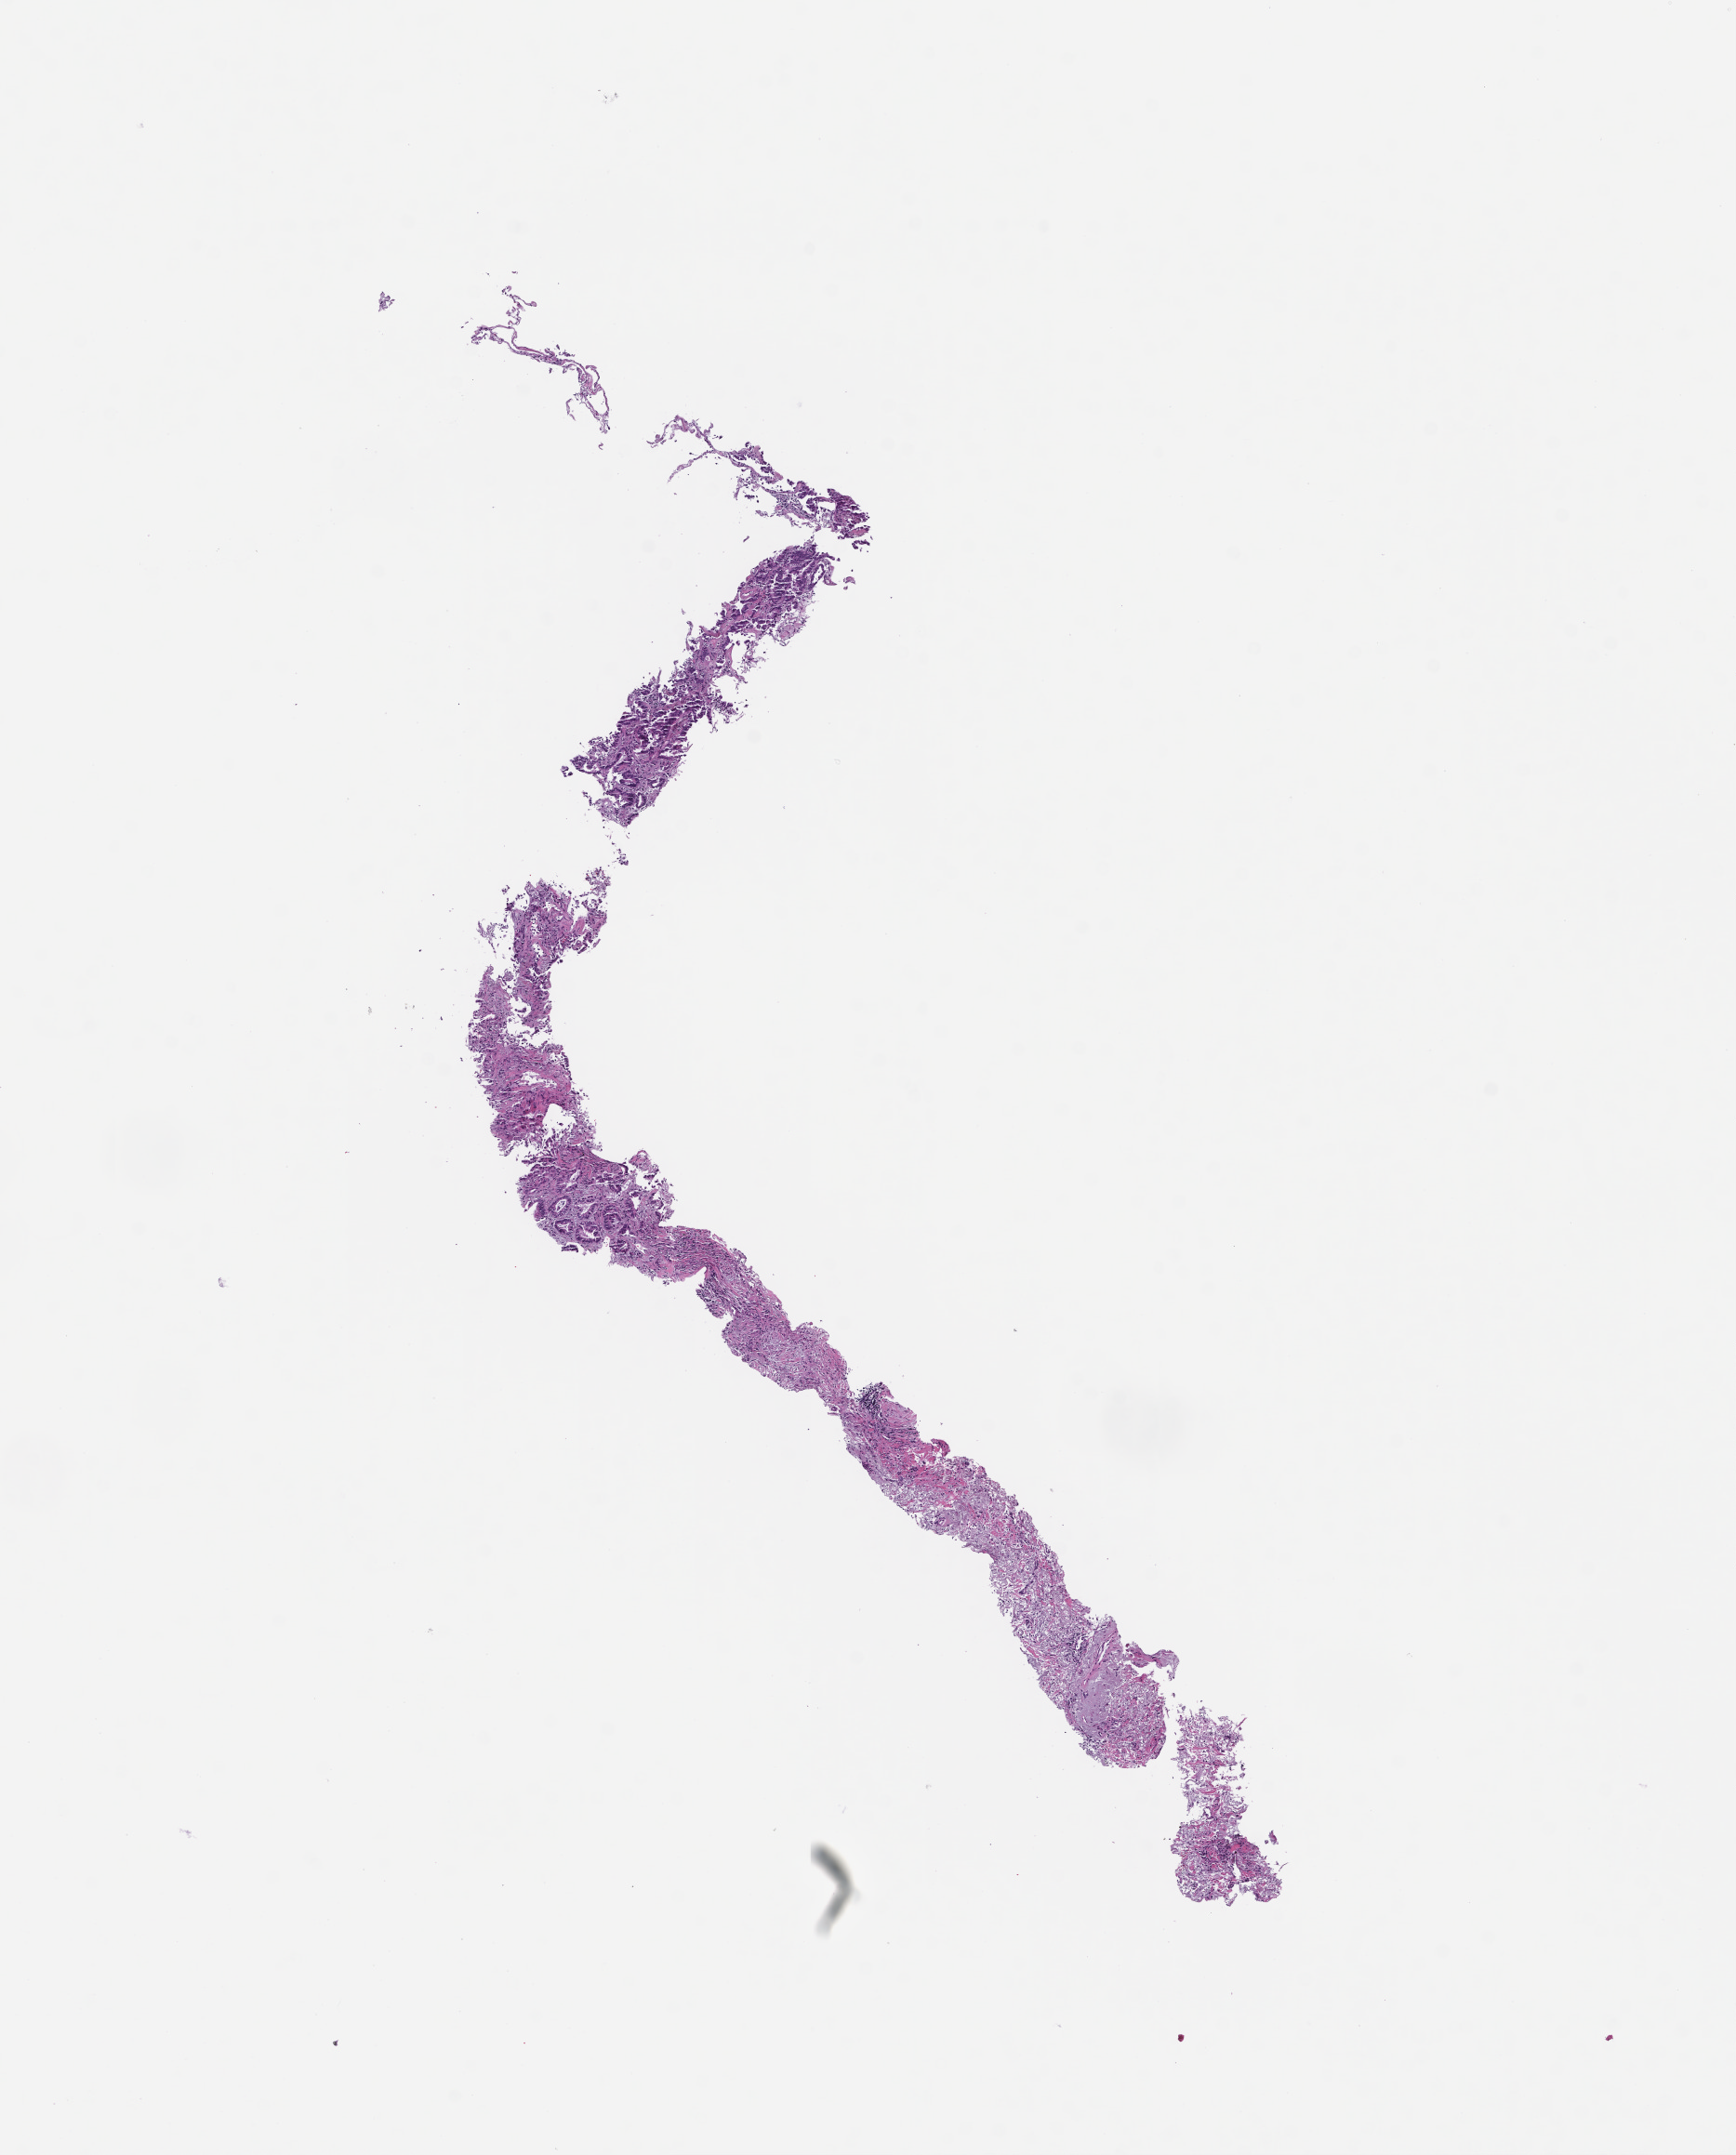
Hematoxylin and eosin (H&E) whole-slide image, low-resolution overview of the scanned area, about 7.5 x 9.4 mm; FFPE section; tissue site: lung. Patient sex: female.
This section: primary tumour tissue. Diagnosis: Non-Small Cell Lung Carcinoma.